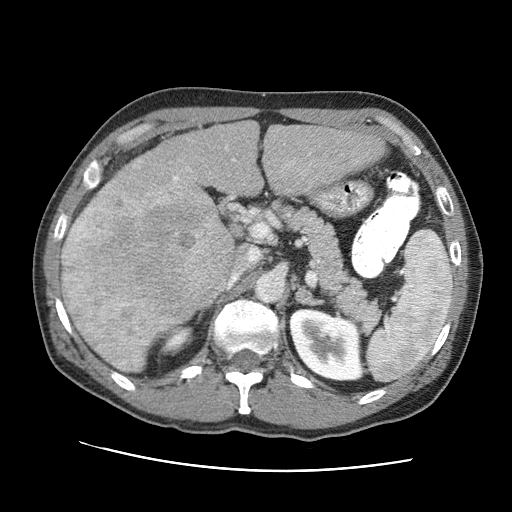
Contrast-enhanced abdominal CT (liver protocol), one axial slice. Slice 45 of 95 in the series (ordered by position). Reconstruction kernel STANDARD. 120 kVp. One of 2 acquisitions stored at this slice position. Soft-tissue window (W 400 / L 40 HU). 2.5 mm slice thickness. 512 × 512 image matrix, field of view 360 × 360 mm. From the clinical record (not read from this slice): diagnosis: hepatocellular carcinoma (patient treated with transarterial chemoembolisation; whether this scan precedes or follows treatment is not stated here); TNM stage (as recorded): Stage-IVA; Child-Pugh class: A; tumour differentiation: moderately differentiated.
Annotated regions visible in this slice (semi-automatic segmentation, software-assisted and operator-edited):
- liver parenchyma outside the tumour (the mass and vessels are separate outlines, so this box may not span the whole liver): bounding box [x1, y1, x2, y2] px = [72, 120, 384, 269]
- mass: [61, 159, 235, 370]
- liver vessels: [107, 146, 310, 188]